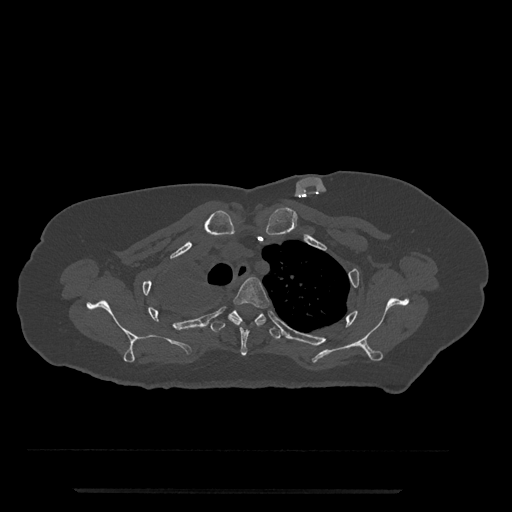
CT including the spine, one axial slice. Position 616 of 797 along the scan axis. Reconstruction kernel Br40s/3. 120 kVp. Bone window (W 1800 / L 400 HU). 512 × 512 image matrix, field of view 440 × 440 mm. Patient: female, 51 years. Case-level facts recorded for this patient, not image findings: primary cancer: neuro; vertebrae with lytic lesions (as recorded): T8.
Outlined on this slice (semi-automatically segmented with operator editing):
- T3 vertebra: bounding box [x1, y1, x2, y2] px = [218, 277, 270, 356]
- T4 vertebra: [210, 310, 281, 339]